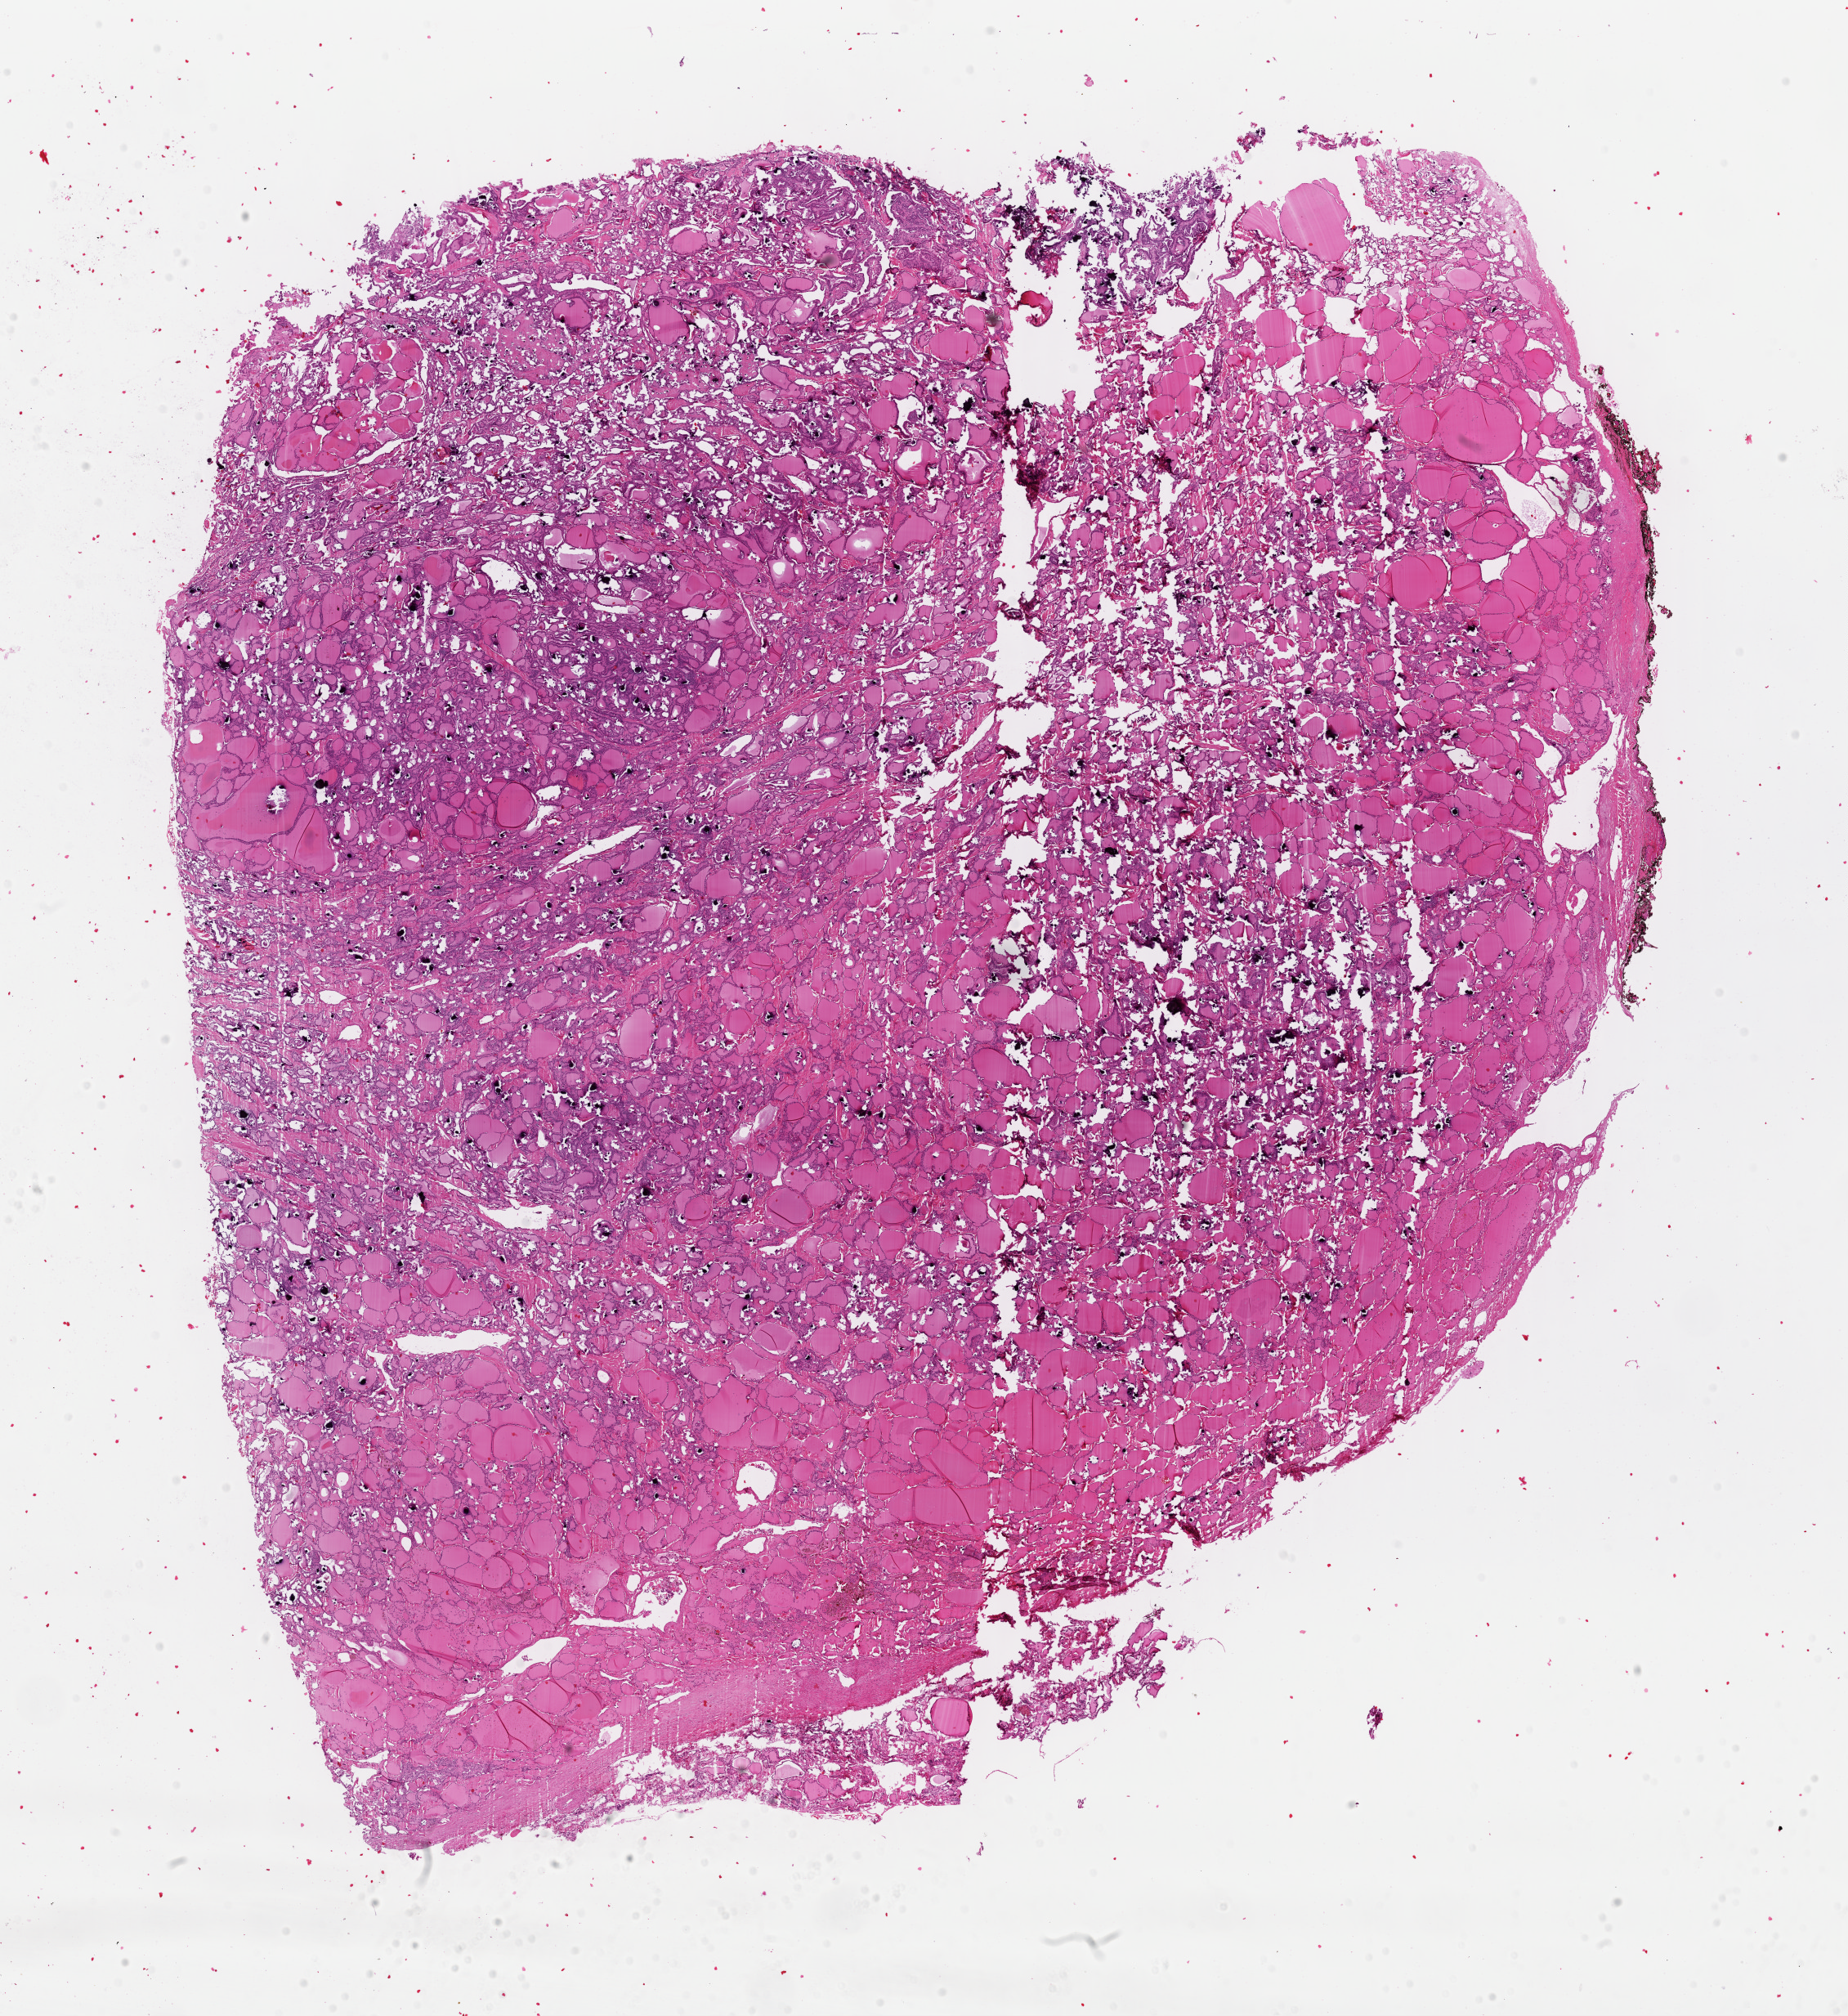
Digitized H&E tissue section (whole slide) — shown as a low-resolution overview of the whole scanned area (about 17.9 x 19.5 mm). FFPE section. Thyroid, primary tumour sample. Male patient; age at initial diagnosis 38 years.
AJCC pathologic stage: I (6th edition). Diagnosis: Papillary carcinoma, follicular variant (thyroid gland). Lymph nodes positive (case pathology): 0 of 3 examined.